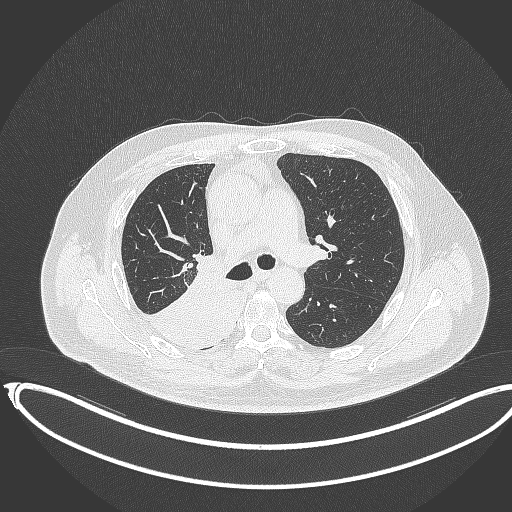
Chest CT, one axial slice; position 229 of 403 along the scan axis; reconstruction kernel B70f; 120 kVp; lung window (W 1500 / L -600 HU); 1 mm slice thickness; 512 × 512 image matrix. Male patient, age 68 years. Case-level facts recorded for this patient, not image findings: clinical TNM (as recorded): T2a N0 M0.
Outlined on this slice (rectangle marked by the reading radiologist):
- lung tumour (recorded histology: adenocarcinoma): box from (x=148, y=257) to (x=237, y=353) px